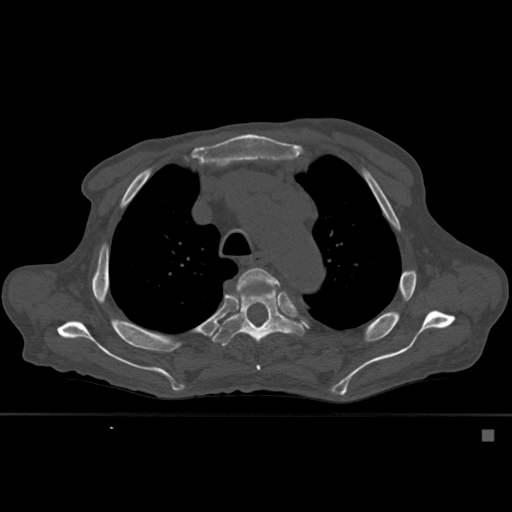
CT including the spine, one axial slice; position 406 of 527 along the scan axis; bone window (W 1800 / L 400 HU); 1.5 mm slice thickness; 512 × 512 image matrix, field of view 373 × 373 mm. Patient: male, 78 years. From the clinical record (not read from this slice): primary cancer: prostate.
Structures marked on this image (semi-automatically segmented with operator editing):
- T4 vertebra: bounding box (x1, y1, x2, y2) in pixels: (232, 268, 279, 371)
- T5 vertebra: (212, 268, 306, 346)